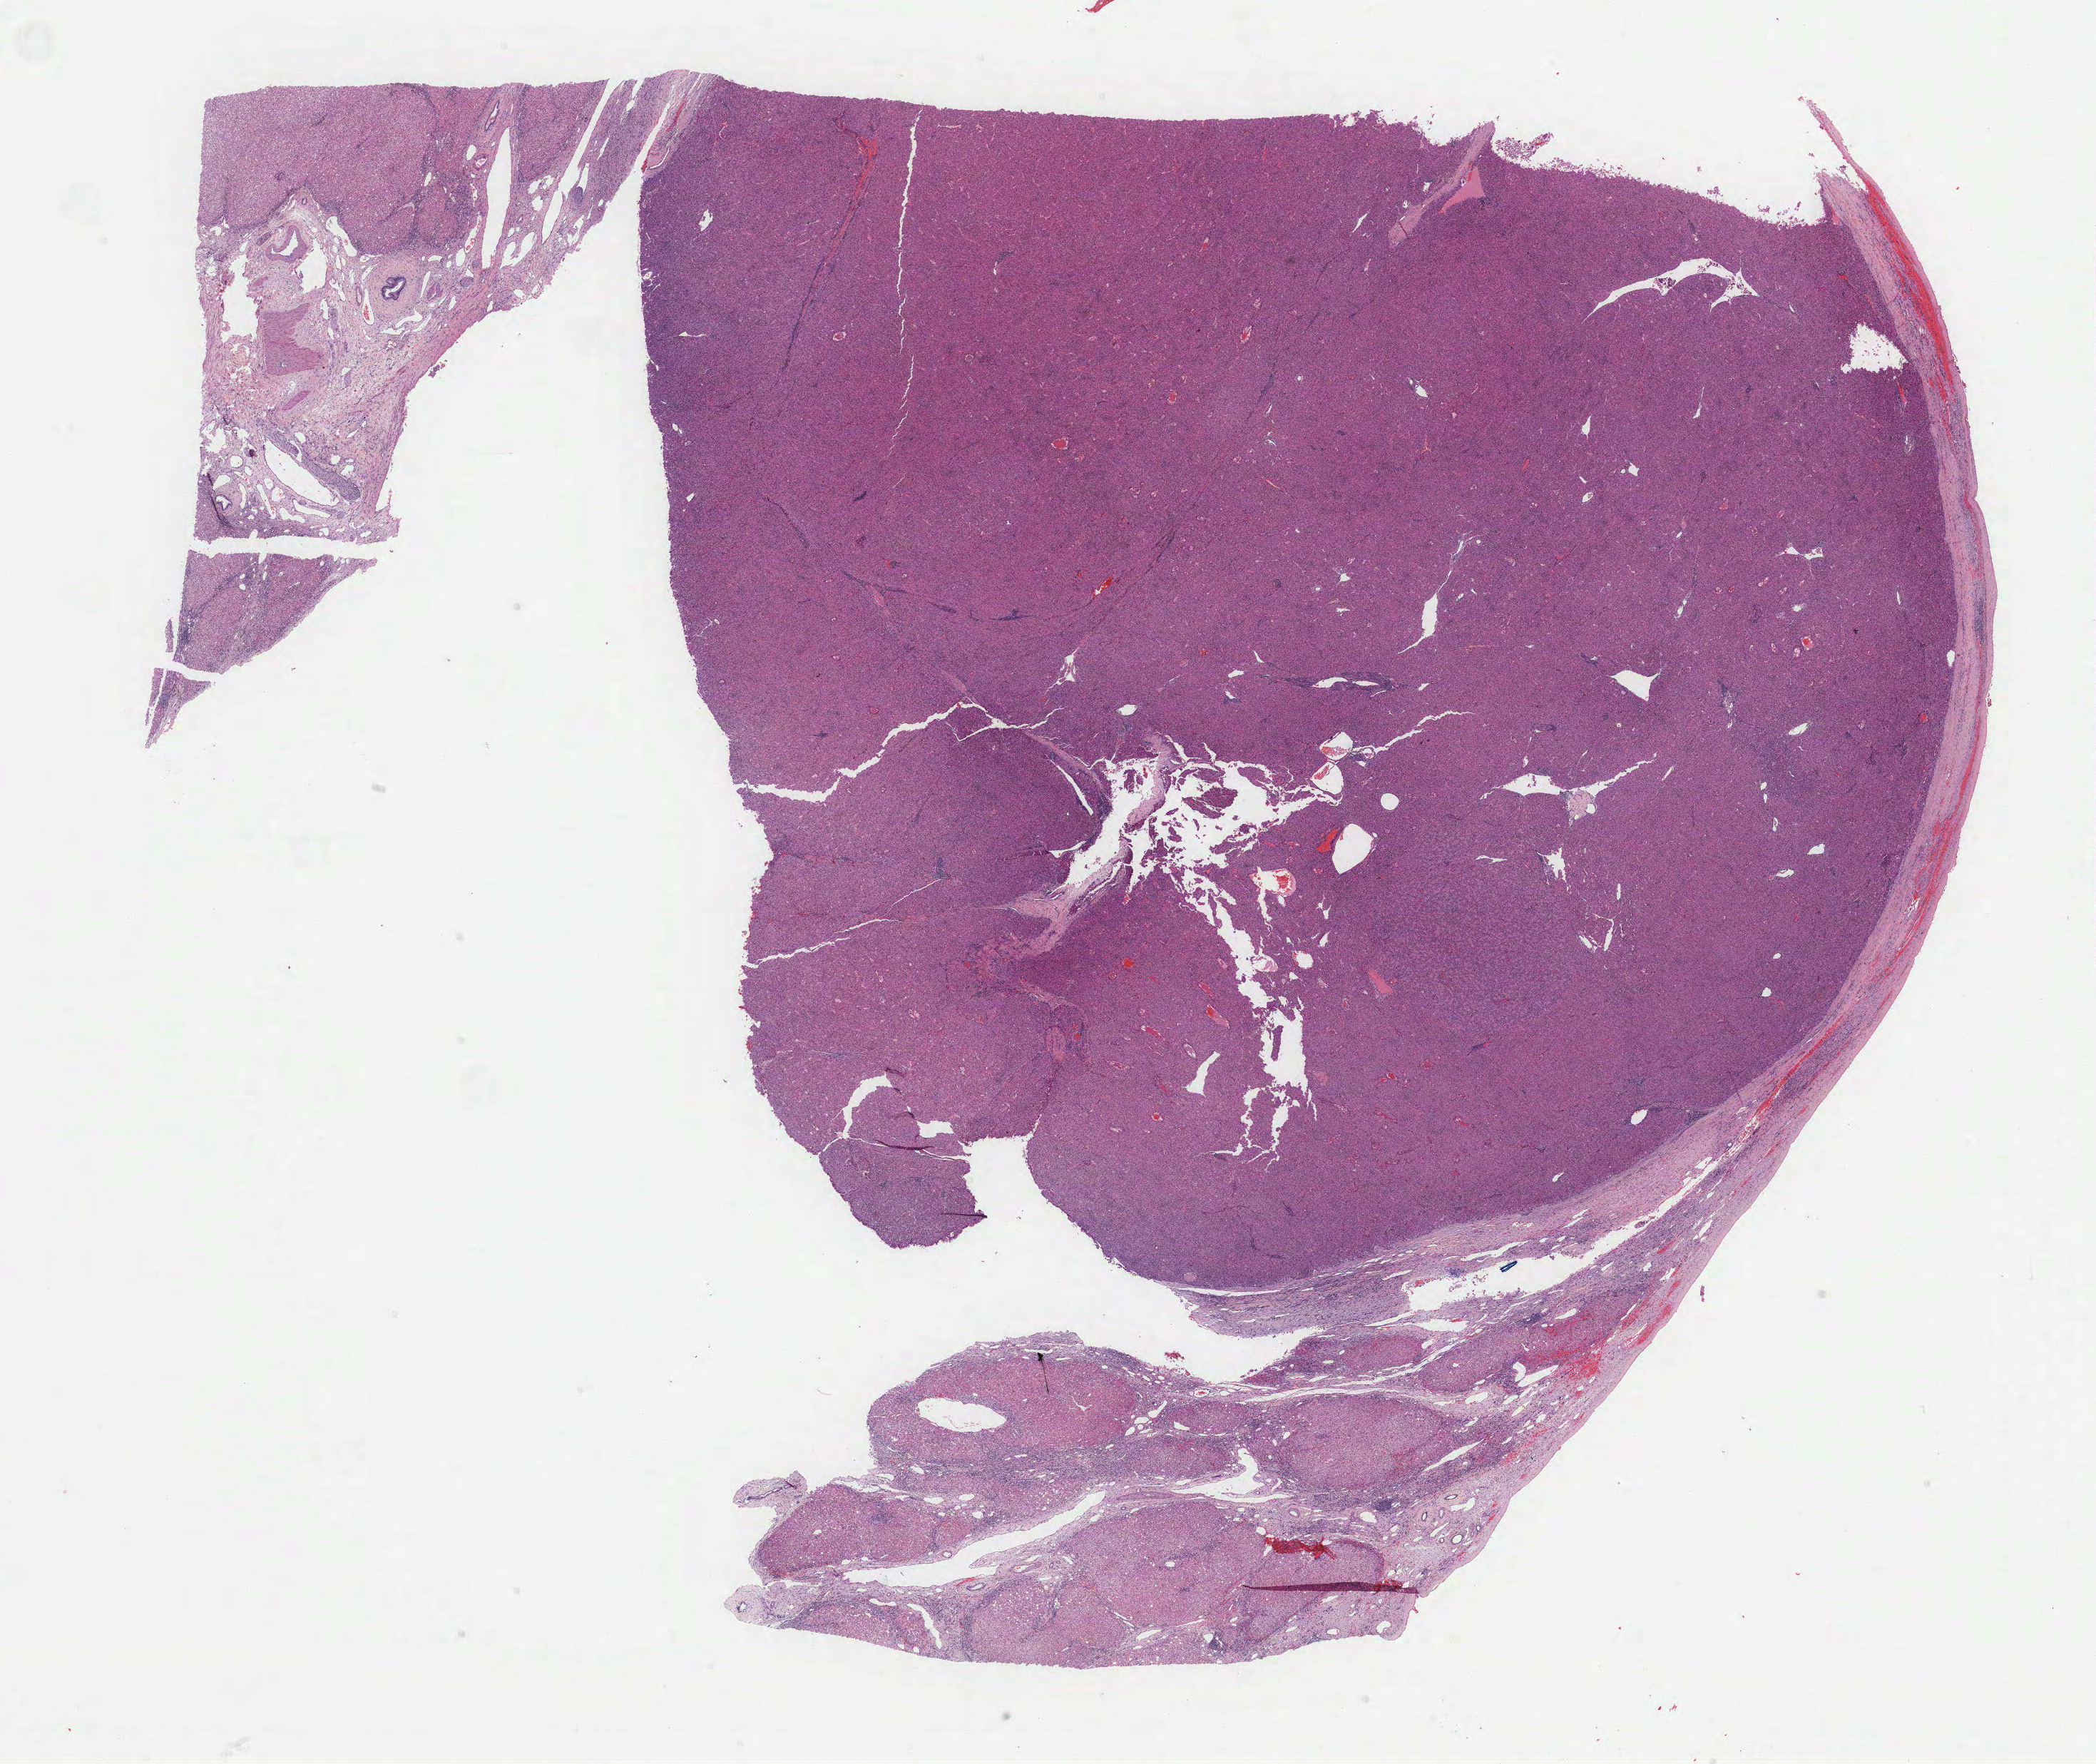
Digitized H&E tissue section (whole slide), shown as a low-resolution overview of the whole scanned area (about 23.7 x 20.0 mm, from a 40x scan); formalin-fixed paraffin-embedded (FFPE) diagnostic section; primary tumour sample from the liver. Patient: male, age at initial diagnosis 66 years. Histologic grade: G2 (moderately differentiated).
AJCC pathologic stage: I (7th edition). Diagnosis: Hepatocellular carcinoma, NOS.